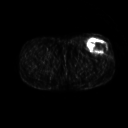
FDG PET of an extremity soft-tissue mass (from a PET/CT study), one axial slice; 128 × 128 image matrix, field of view 500 × 500 mm. Patient: male, 64 years. Case-level facts recorded for this patient, not image findings: histological type: extraskeletal osteosarcoma; grade: high; site of the primary tumour: thigh.
Structures marked on this image (expert contour drawn on MRI and transferred to this co-registered scan by the dataset authors):
- gross tumour volume (mass): bounding box <87,39,108,53> (left, top, right, bottom; pixels)